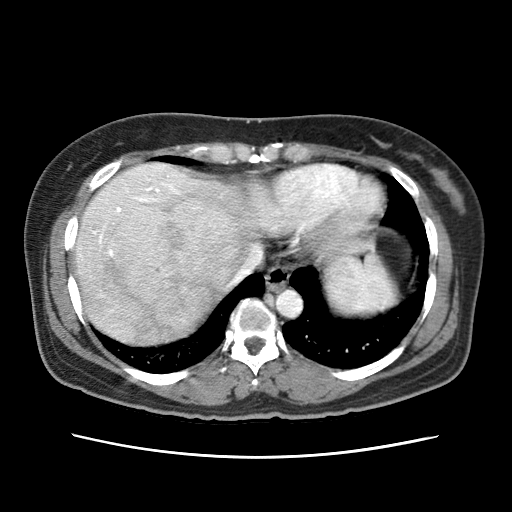
Contrast-enhanced abdominal CT (liver protocol), one axial slice. Position 59 of 79 along the scan axis. 120 kVp. Soft-tissue window (W 400 / L 40 HU). 2.5 mm slice thickness. 512 × 512 image matrix, field of view 340 × 340 mm. From the clinical record (not read from this slice): diagnosis: hepatocellular carcinoma (patient treated with transarterial chemoembolisation; whether this scan precedes or follows treatment is not stated here); TNM stage (as recorded): Stage-I; Child-Pugh class: A.
Annotated regions visible in this slice (semi-automatically segmented with operator editing):
- abdominal aorta: bounding box <274,289,302,318> (left, top, right, bottom; pixels)
- liver parenchyma outside the tumour (the mass and vessels are separate outlines, so this box may not span the whole liver): <74,162,296,344>
- mass: <103,196,241,312>
- liver vessels: <93,165,179,254>